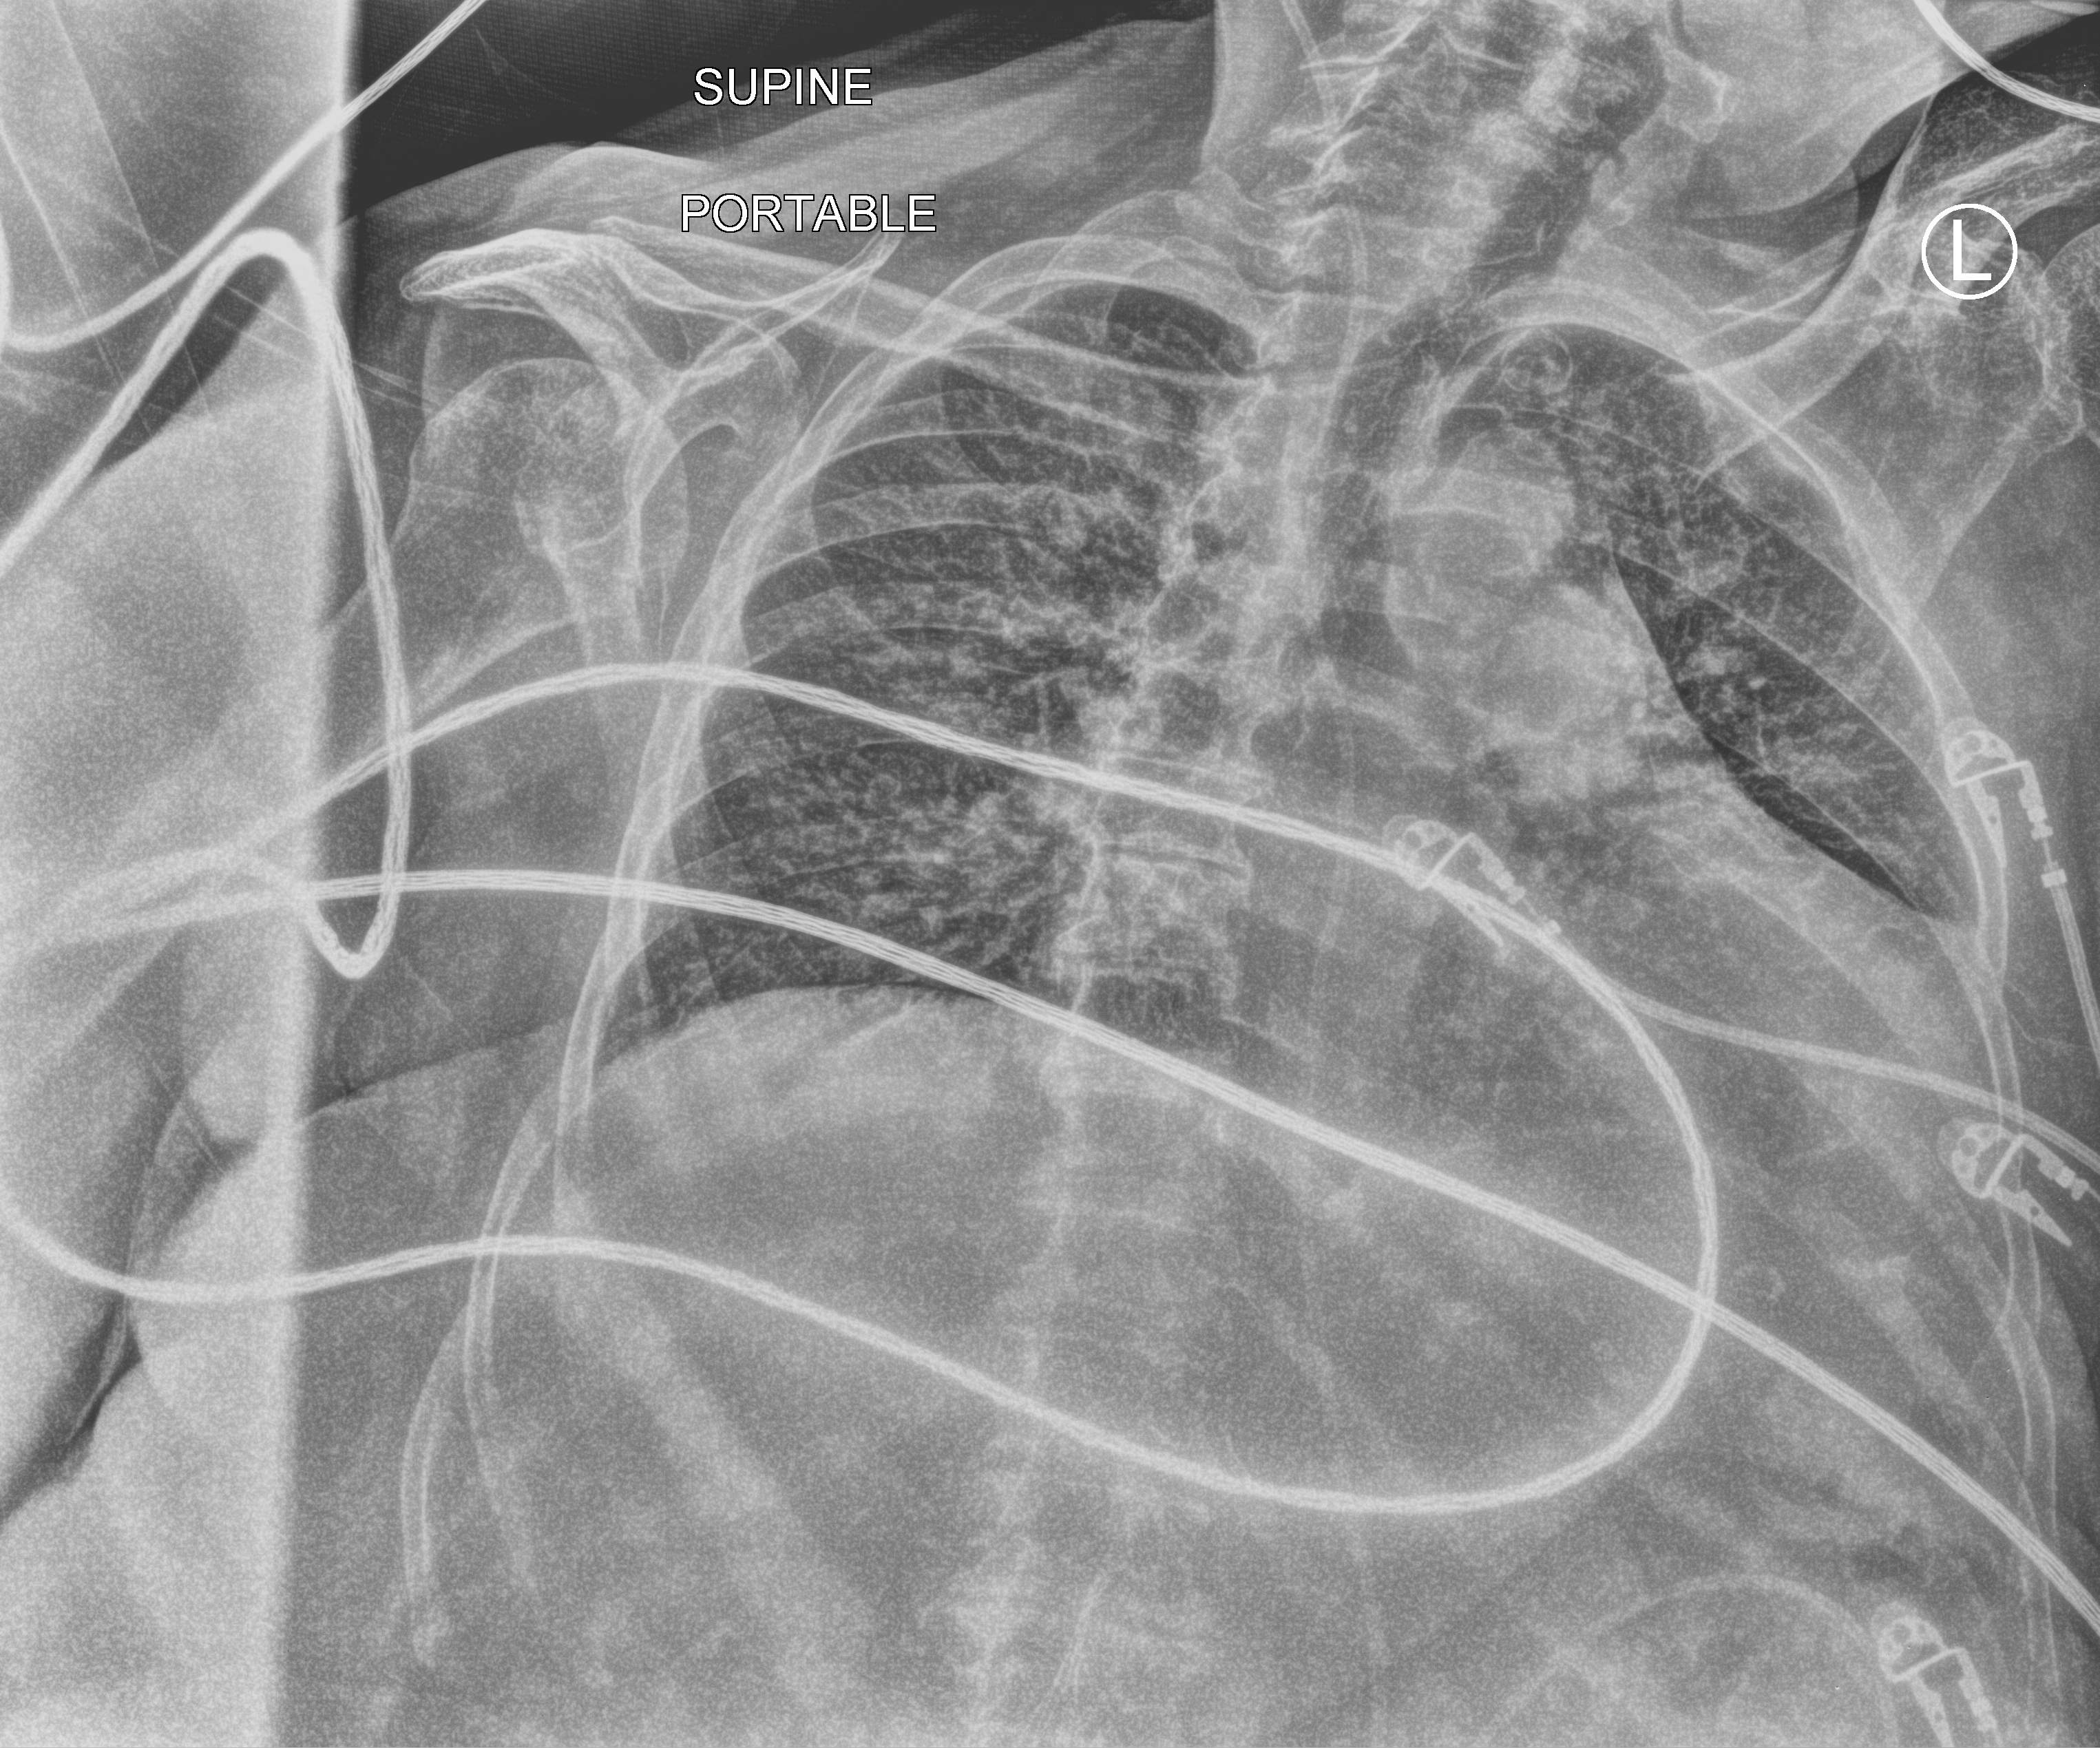
Bedside chest radiograph (computed radiography); anteroposterior (AP) projection. Patient hospitalised with COVID-19; female, aged 75–90 years.
From the hospital-stay record, not from the radiograph (when in the stay this image was taken is not recorded):
- admitted to intensive care during this hospital stay: yes
- mechanically ventilated during this hospital stay: yes